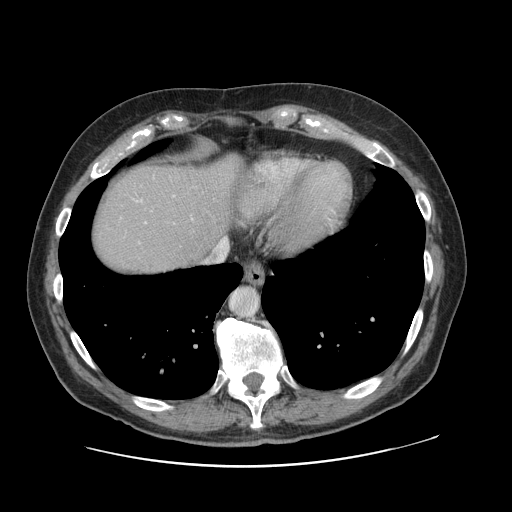
Contrast-enhanced abdominal CT, one axial slice; slice 106 of 138 in the series (ordered by position); 120 kVp; intravenous contrast given; soft-tissue window (W 400 / L 40 HU); 512 × 512 image matrix. Male patient, age 71 years. From the clinical record (not read from this slice): diagnosis: colorectal cancer liver metastases, imaged before liver resection; multiple liver metastases: no; largest metastasis: 3.3 cm; chemotherapy before resection: no.
Outlined on this slice (manually delineated by an expert):
- hepatic veins: box from (x=204, y=237) to (x=228, y=264) px
- liver: (x=91, y=156)–(x=242, y=276)
- planned liver remnant (the part of the liver to remain after resection): (x=92, y=165)–(x=223, y=276)